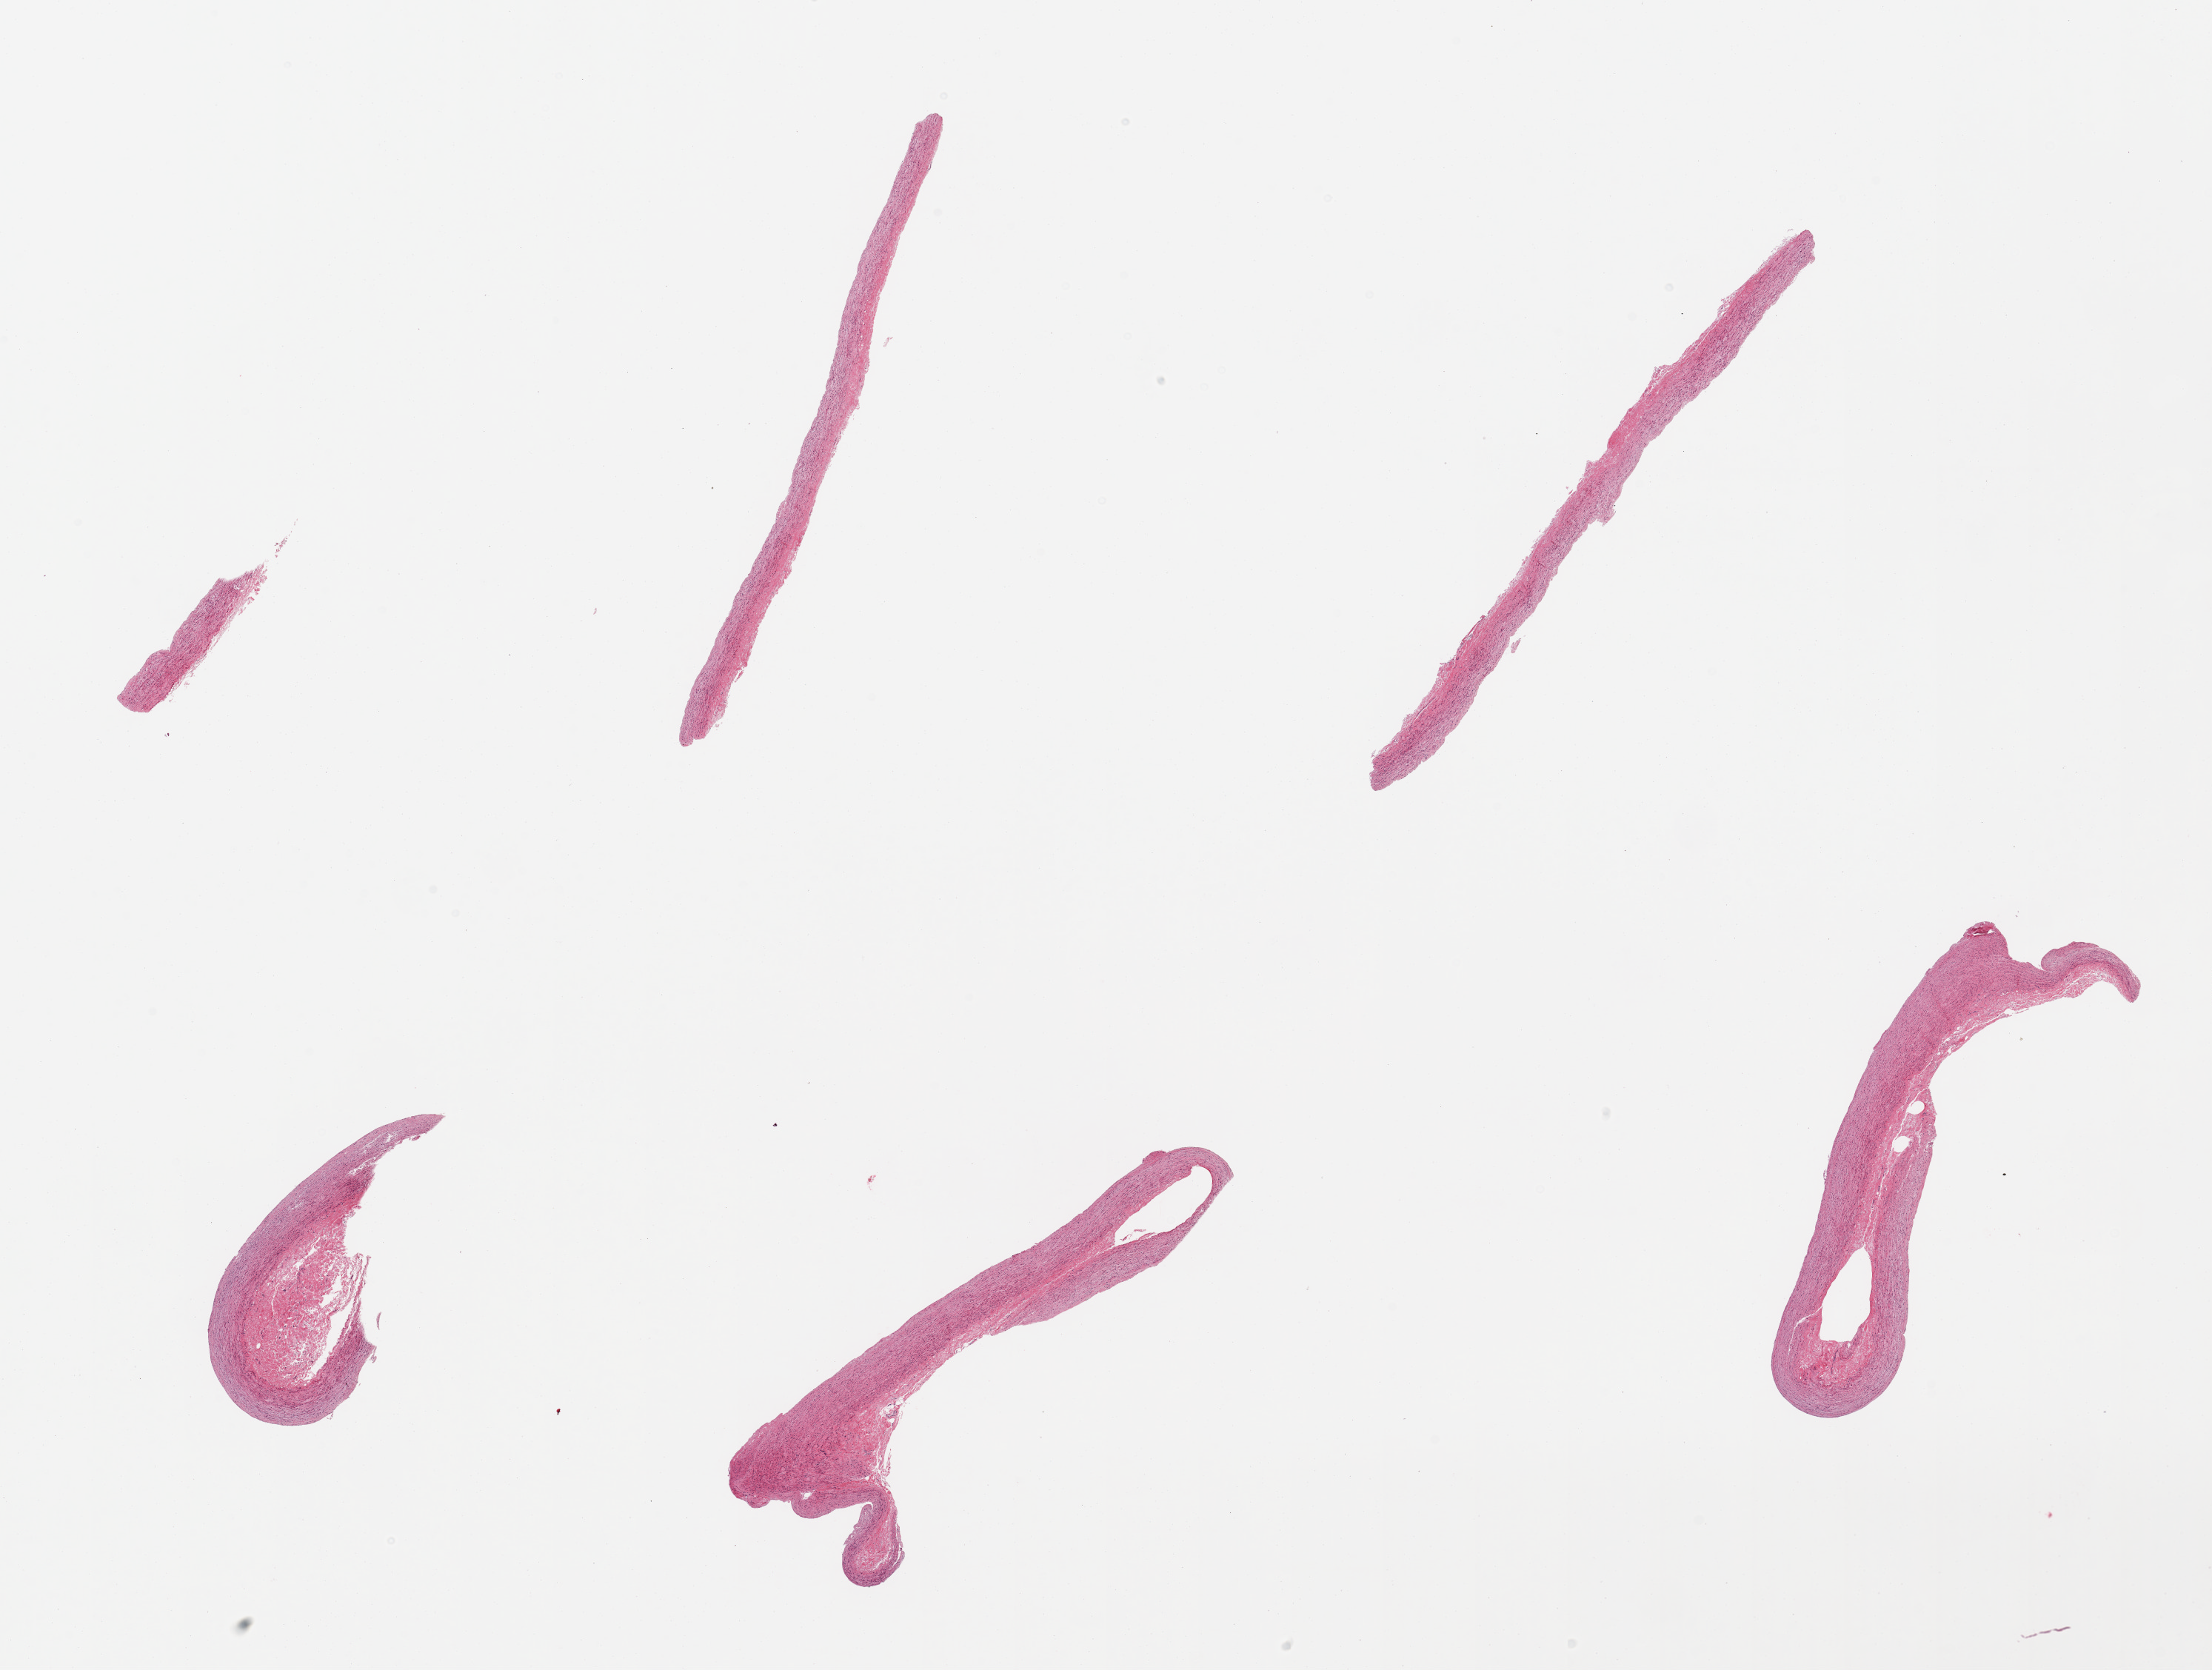
H&E whole-slide image, brightfield, a low-resolution overview of the entire scanned area, about 23.6 x 17.8 mm, PAXgene-fixed paraffin-embedded (PFPE) section, target tissue: aorta, tissue donor sample. Male donor.
• reviewer comment on this tissue sample: 6 pieces